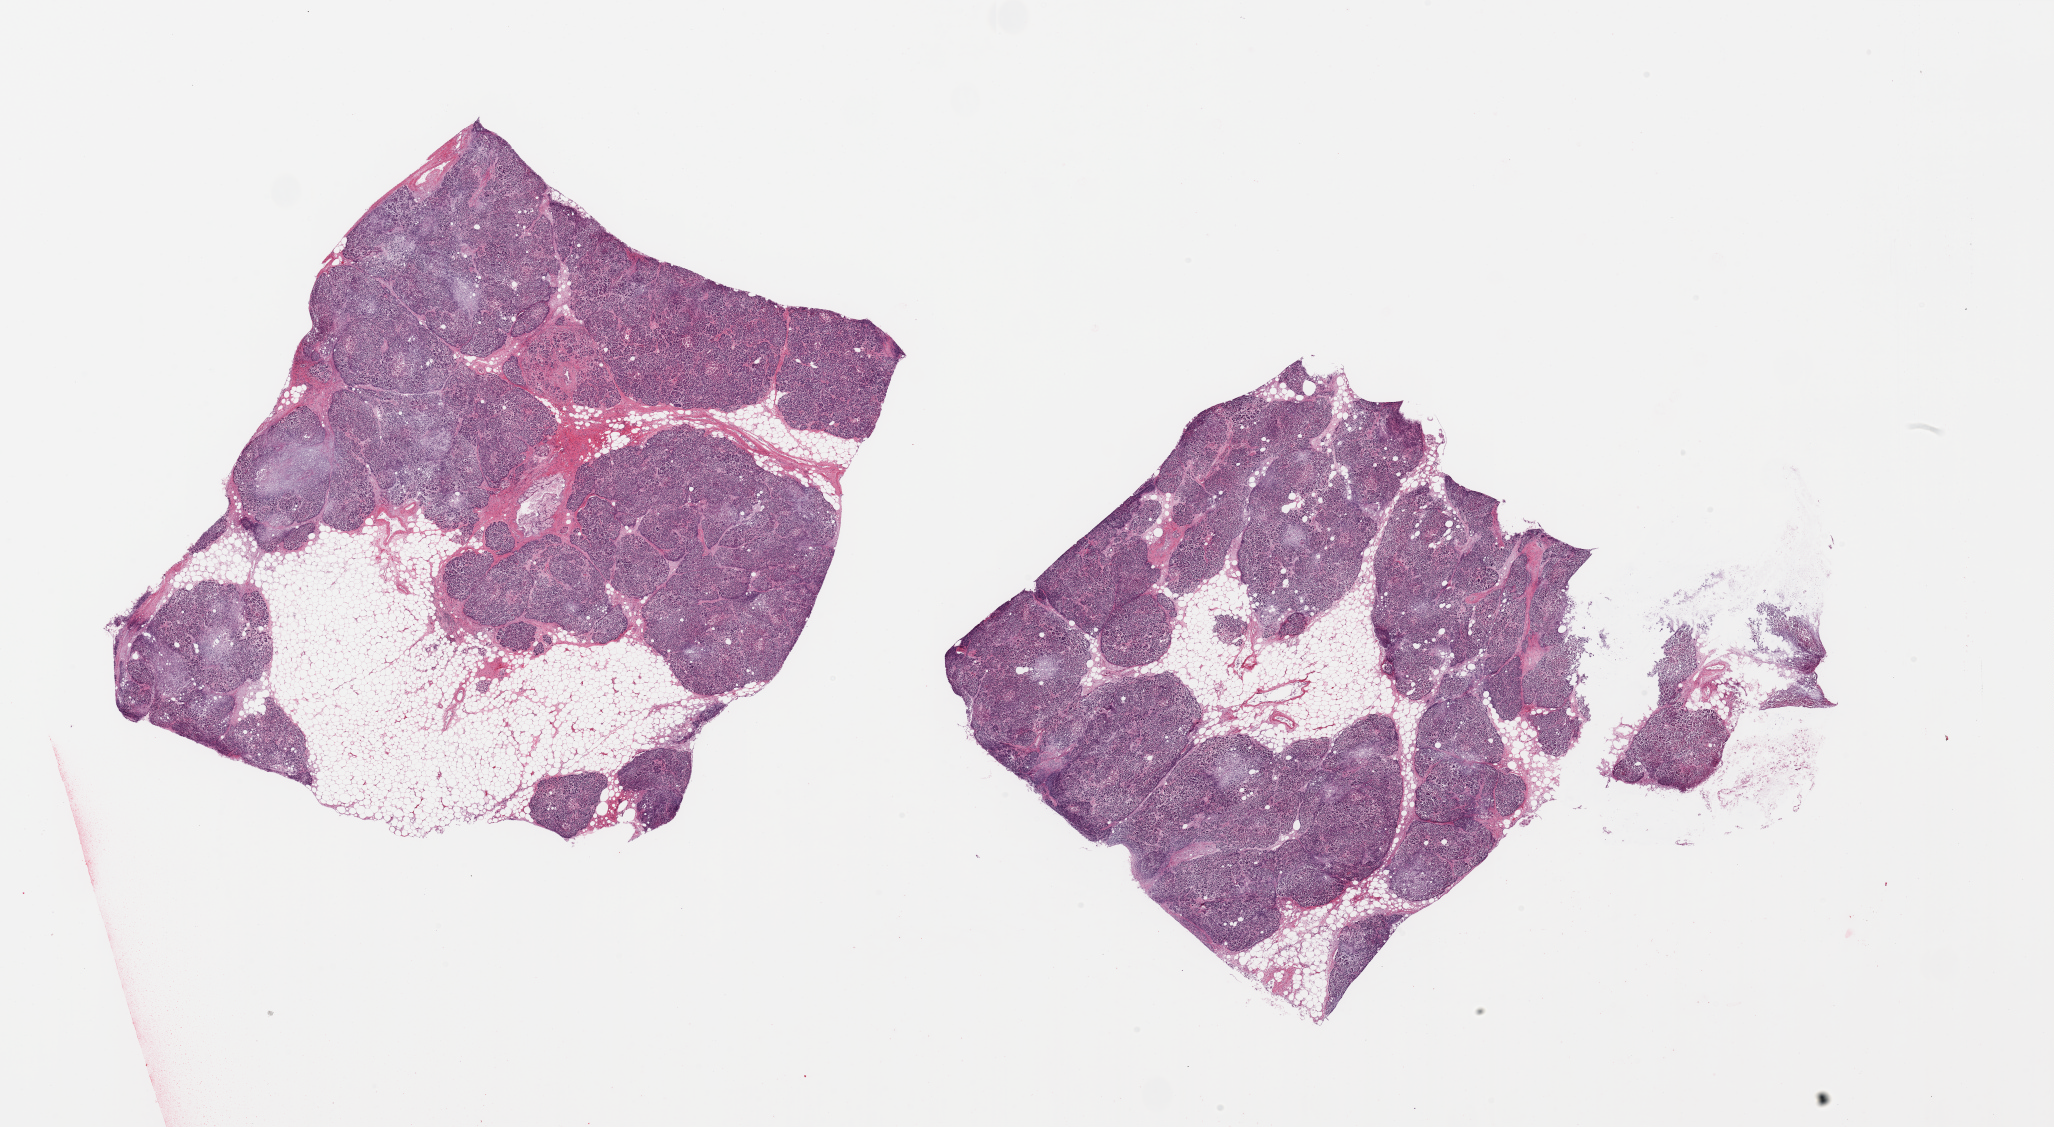
Digitized haematoxylin and eosin-stained section, low-resolution overview of the scanned area, about 32.5 x 17.8 mm; PAXgene-fixed paraffin-embedded (PFPE) section; section of pancreas (target tissue); donor tissue sample. Donor sex: male.
Reviewer comment on this tissue sample: 2 pieces; 40% fat content.